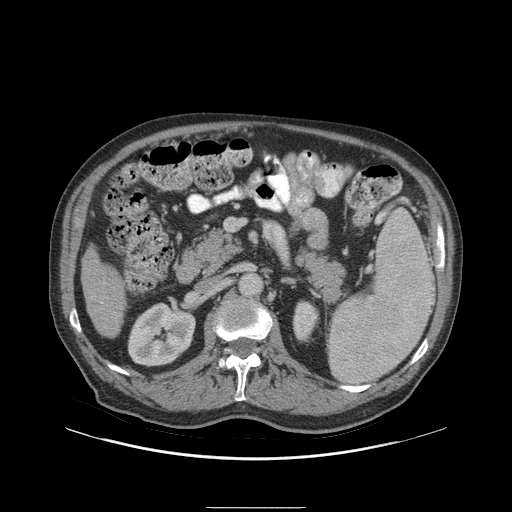
Contrast-enhanced abdominal CT (liver protocol), one axial slice; 140 kVp; soft-tissue window (W 400 / L 40 HU); 2.5 mm slice thickness; 512 × 512 image matrix, field of view 440 × 440 mm. From the clinical record (not read from this slice): diagnosis: hepatocellular carcinoma (patient treated with transarterial chemoembolisation; whether this scan precedes or follows treatment is not stated here); TNM stage (as recorded): Stage-I; Child-Pugh class: A; tumour nodularity: uninodular.
Annotated regions visible in this slice (semi-automatically segmented with operator editing):
- liver parenchyma outside the tumour (the mass and vessels are separate outlines, so this box may not span the whole liver): bounding box (x1, y1, x2, y2) in pixels: (80, 244, 126, 338)